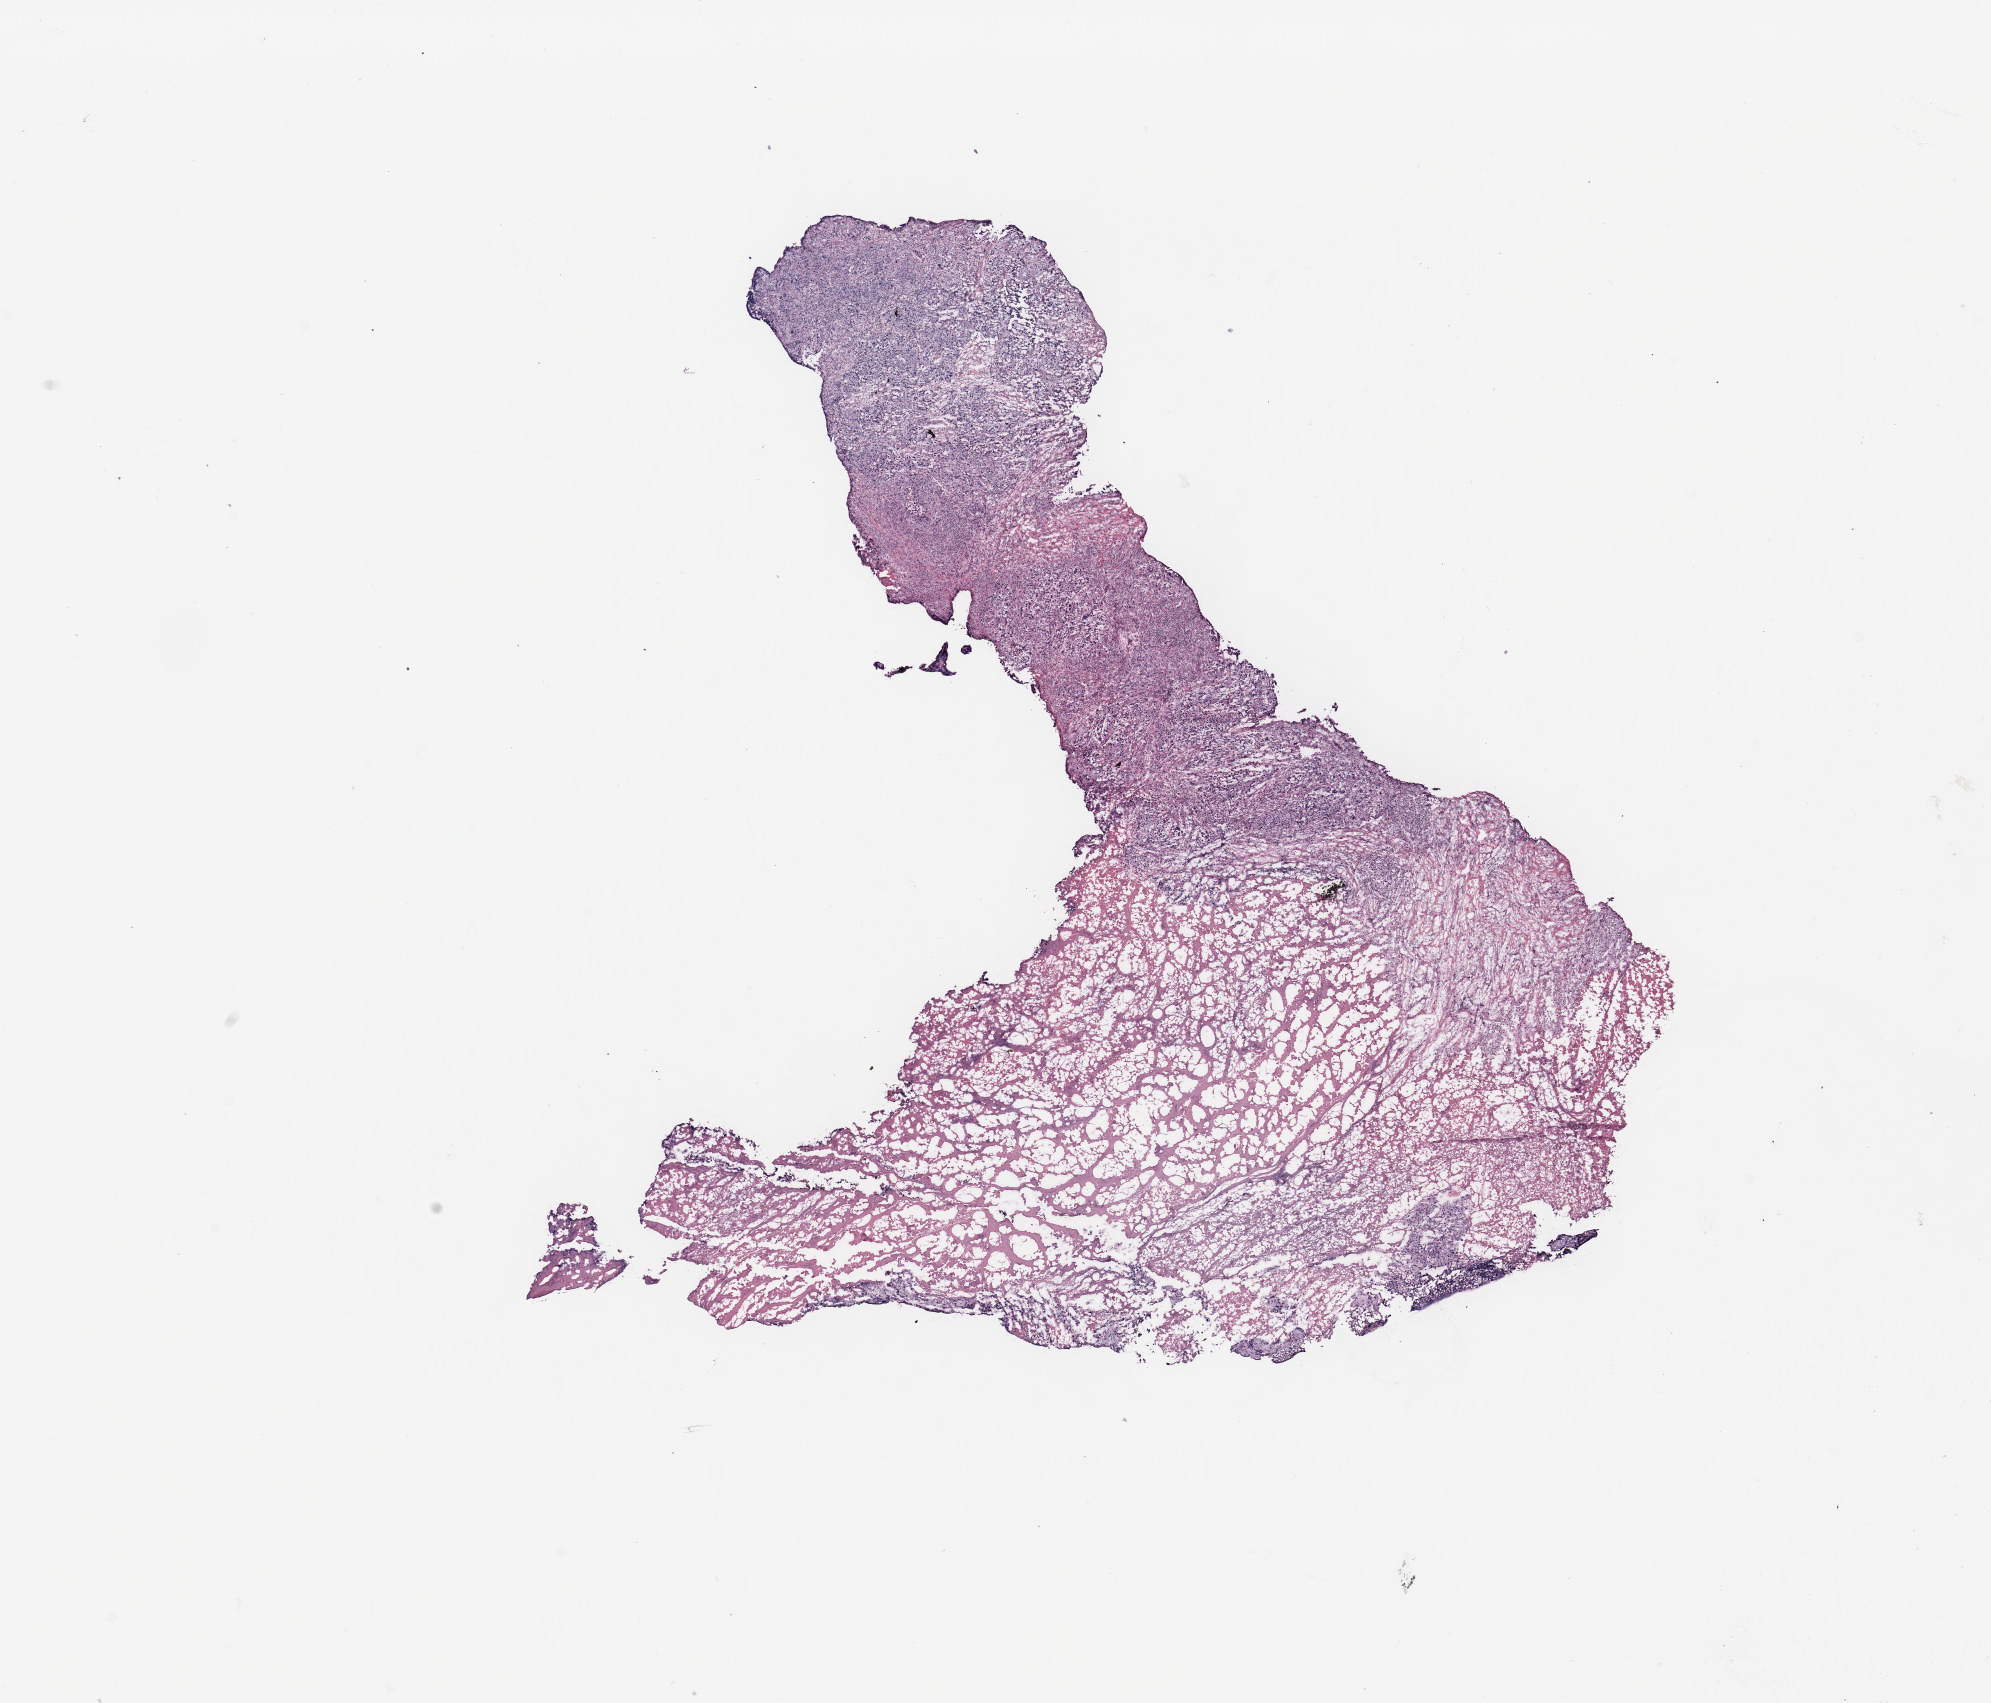
Digitized H&E-stained tissue section (whole slide), shown as a low-resolution overview of the whole scanned area (about 15.8 x 13.5 mm). Breast, tissue type not recorded.
• patient diagnosis (cohort enrolment): breast cancer (breast)